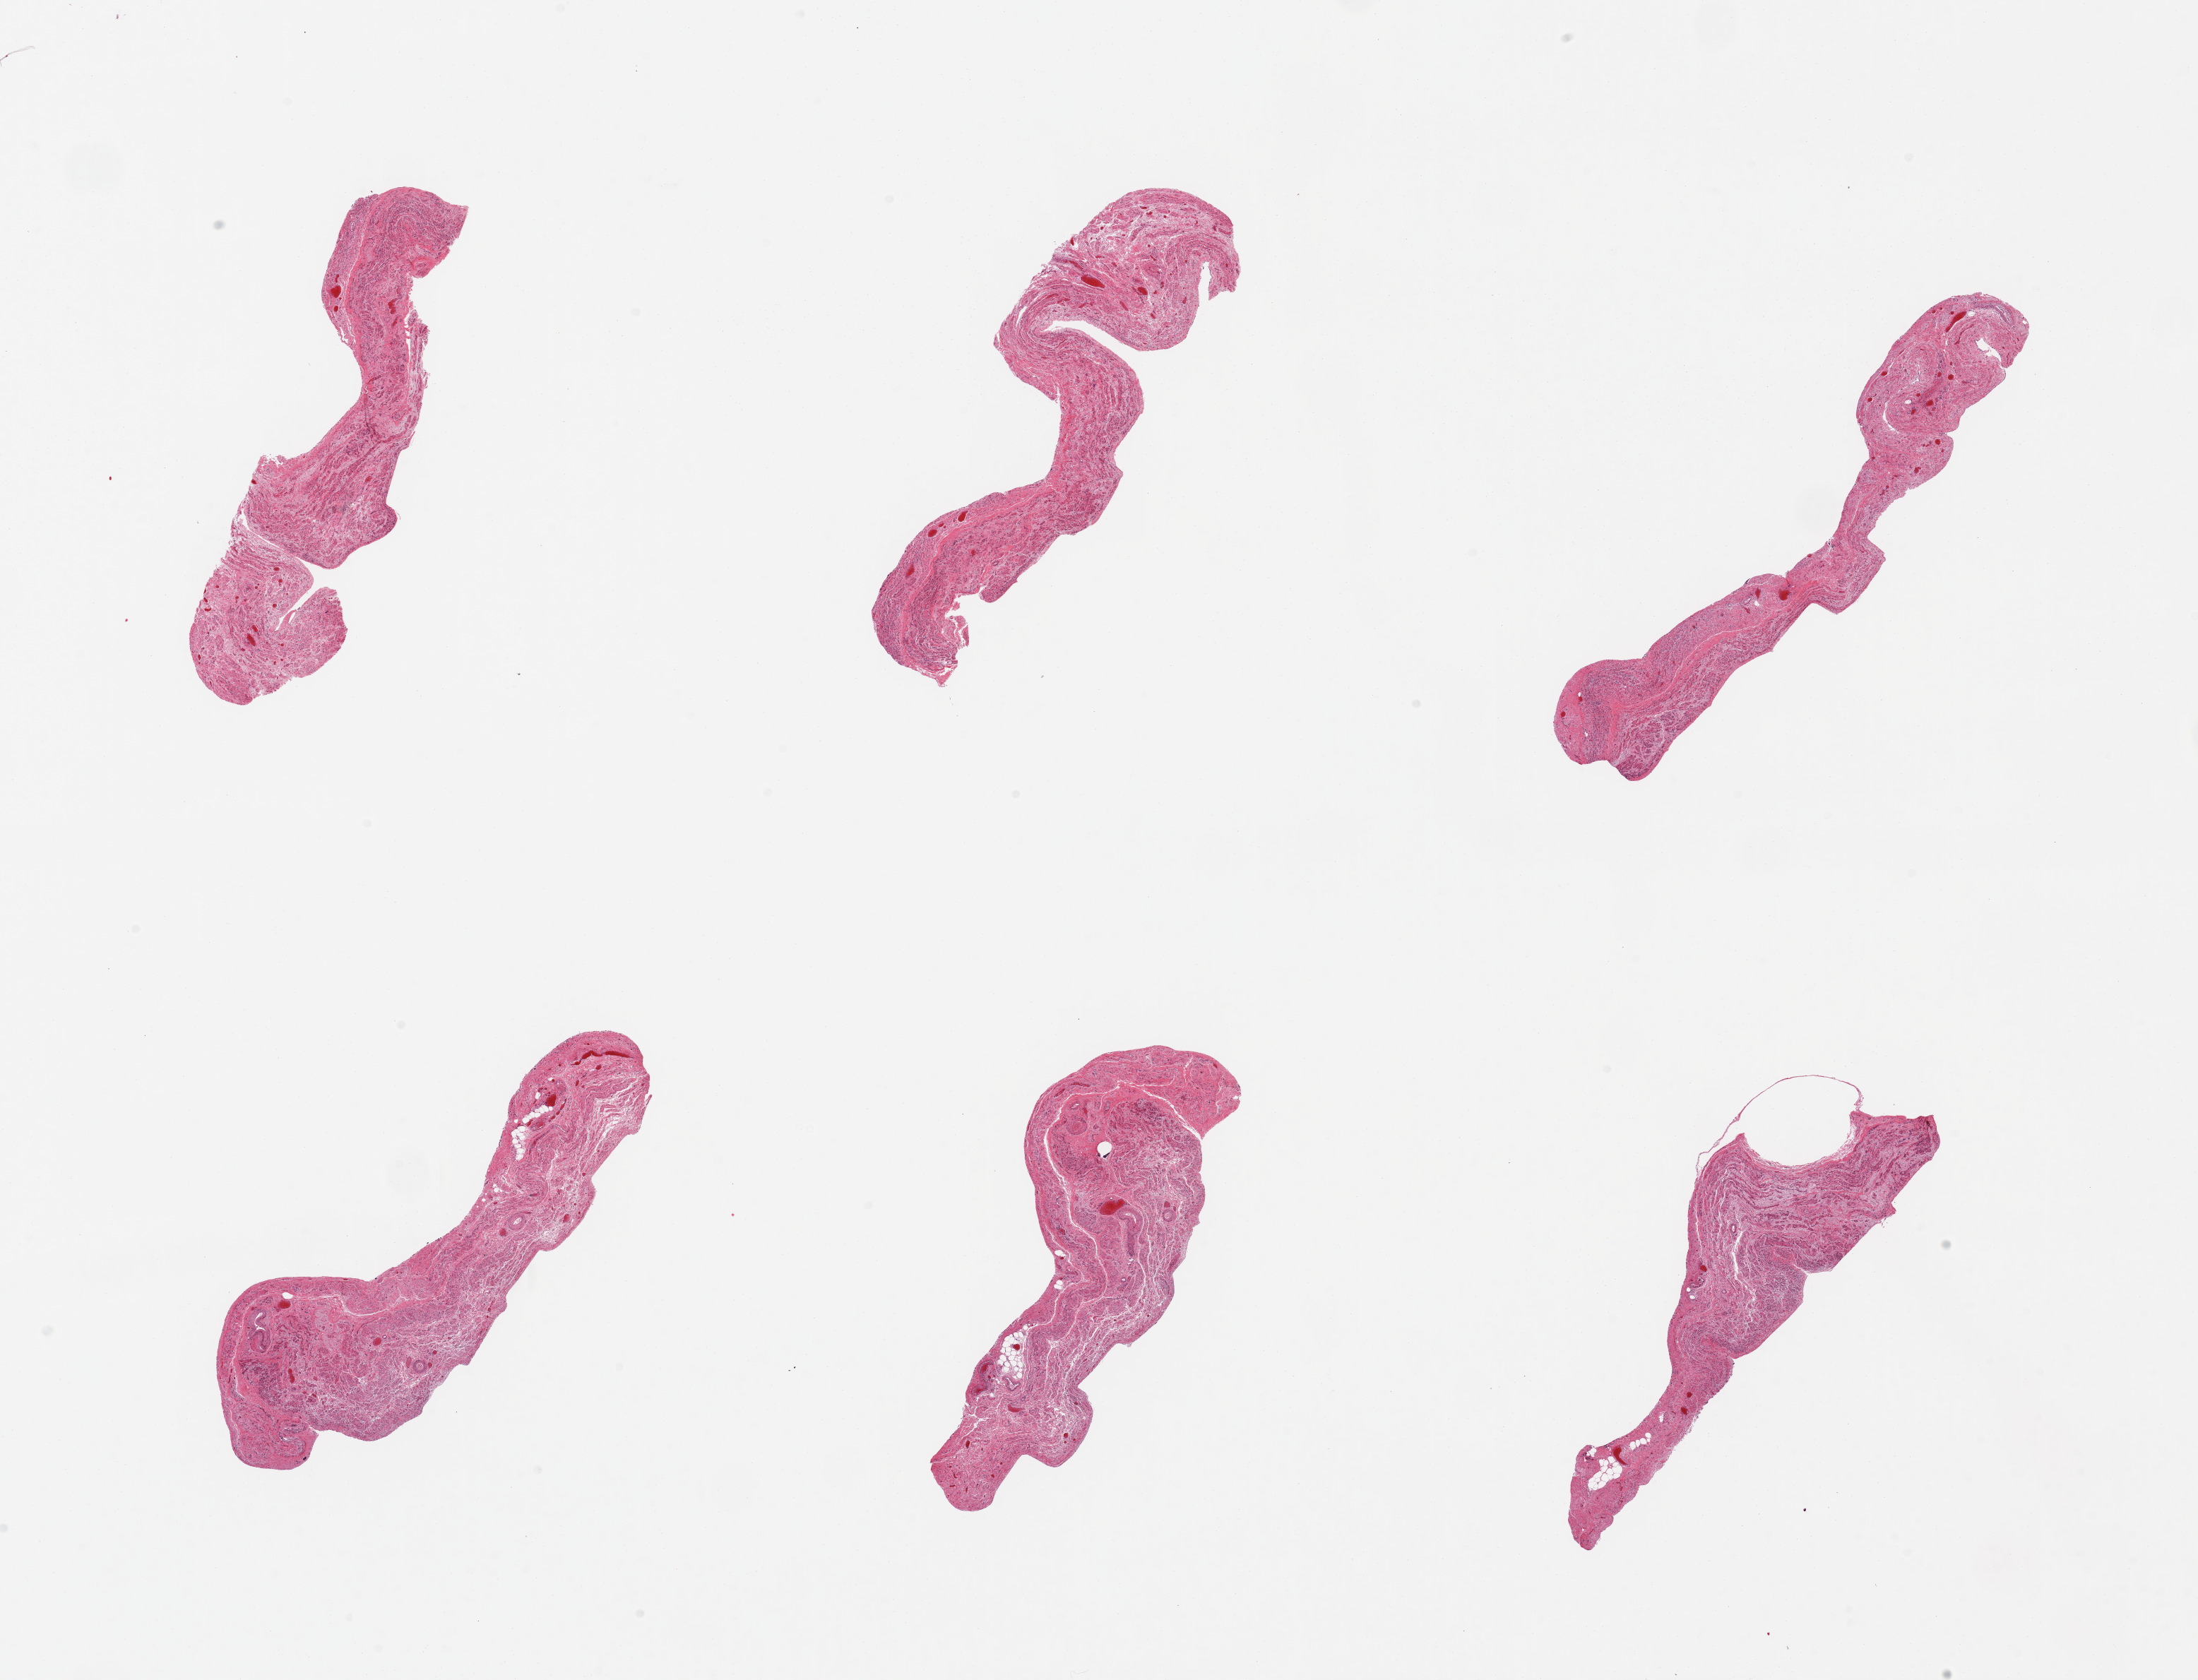
H&E whole-slide image, brightfield — whole scanned area (about 24.6 x 18.8 mm, slide scanned at 20x) shown as a low-resolution overview. PAXgene-fixed, paraffin-embedded tissue. Sampled site (target tissue): vagina. Tissue donor sample. Female donor.
Pathologist's review note for this sample: 6 pieces; no epithelium; smooth muscle does not resemble normal vagina; origin unknown.